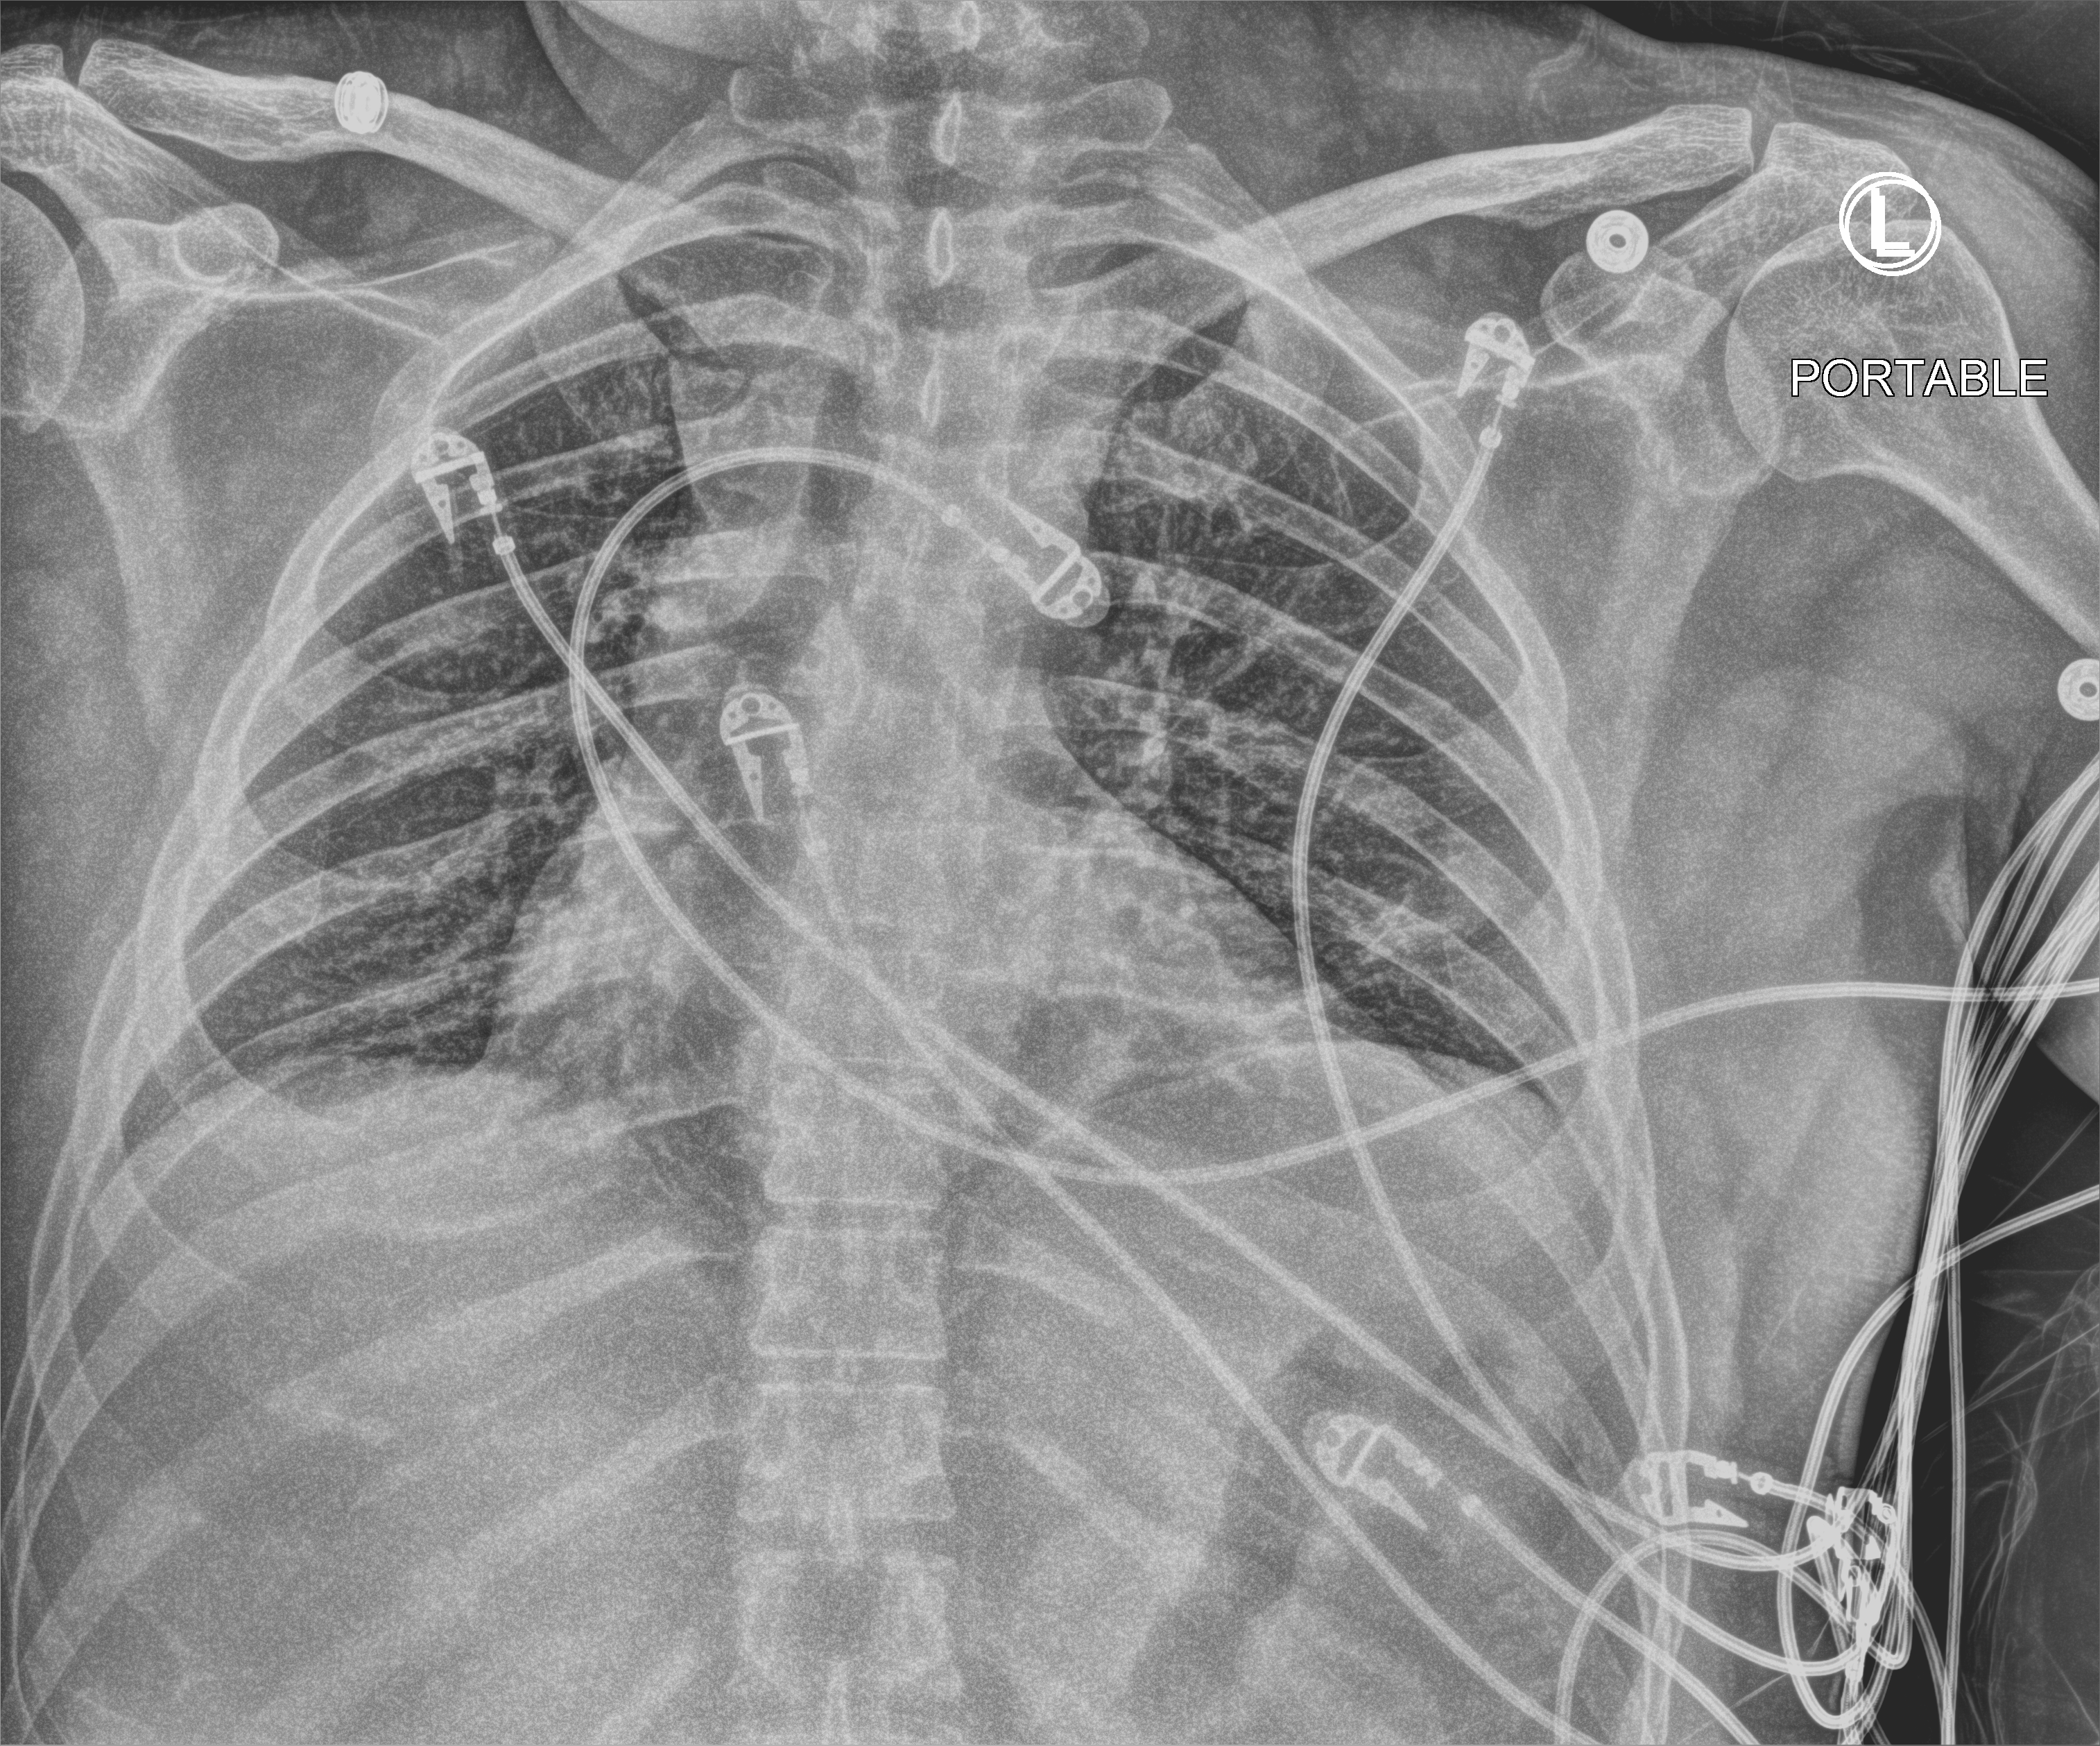
Bedside chest radiograph (computed radiography). Male patient hospitalised with COVID-19, age 18–59 years.
Admission-level facts for this patient (not findings on this image; timing relative to this image not recorded): admitted to intensive care during this hospital stay: yes; mechanically ventilated during this hospital stay: yes.